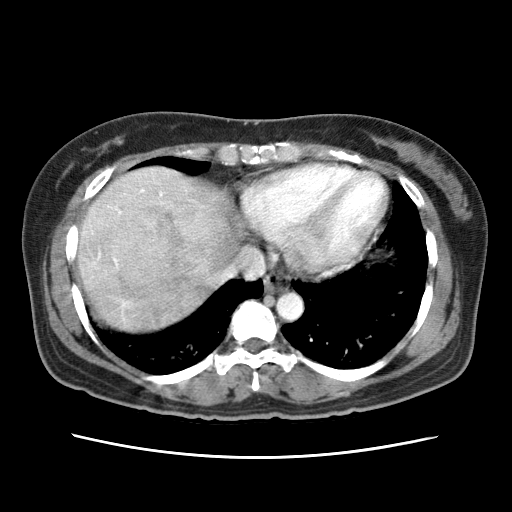
Contrast-enhanced abdominal CT (liver protocol), one axial slice. Position 61 of 79 along the scan axis. Reconstruction kernel STANDARD. 120 kVp. Soft-tissue window (W 400 / L 40 HU). 512 × 512 image matrix. From the clinical record (not read from this slice): diagnosis: hepatocellular carcinoma (patient treated with transarterial chemoembolisation; whether this scan precedes or follows treatment is not stated here); TNM stage (as recorded): Stage-I; Child-Pugh class: A; tumour differentiation: moderately differentiated.
Outlined on this slice (semi-automatically segmented with operator editing):
- abdominal aorta: bounding box [x1, y1, x2, y2] px = [275, 292, 303, 320]
- liver parenchyma outside the tumour (the mass and vessels are separate outlines, so this box may not span the whole liver): [78, 166, 232, 330]
- mass: [114, 203, 228, 296]
- liver vessels: [99, 189, 163, 305]